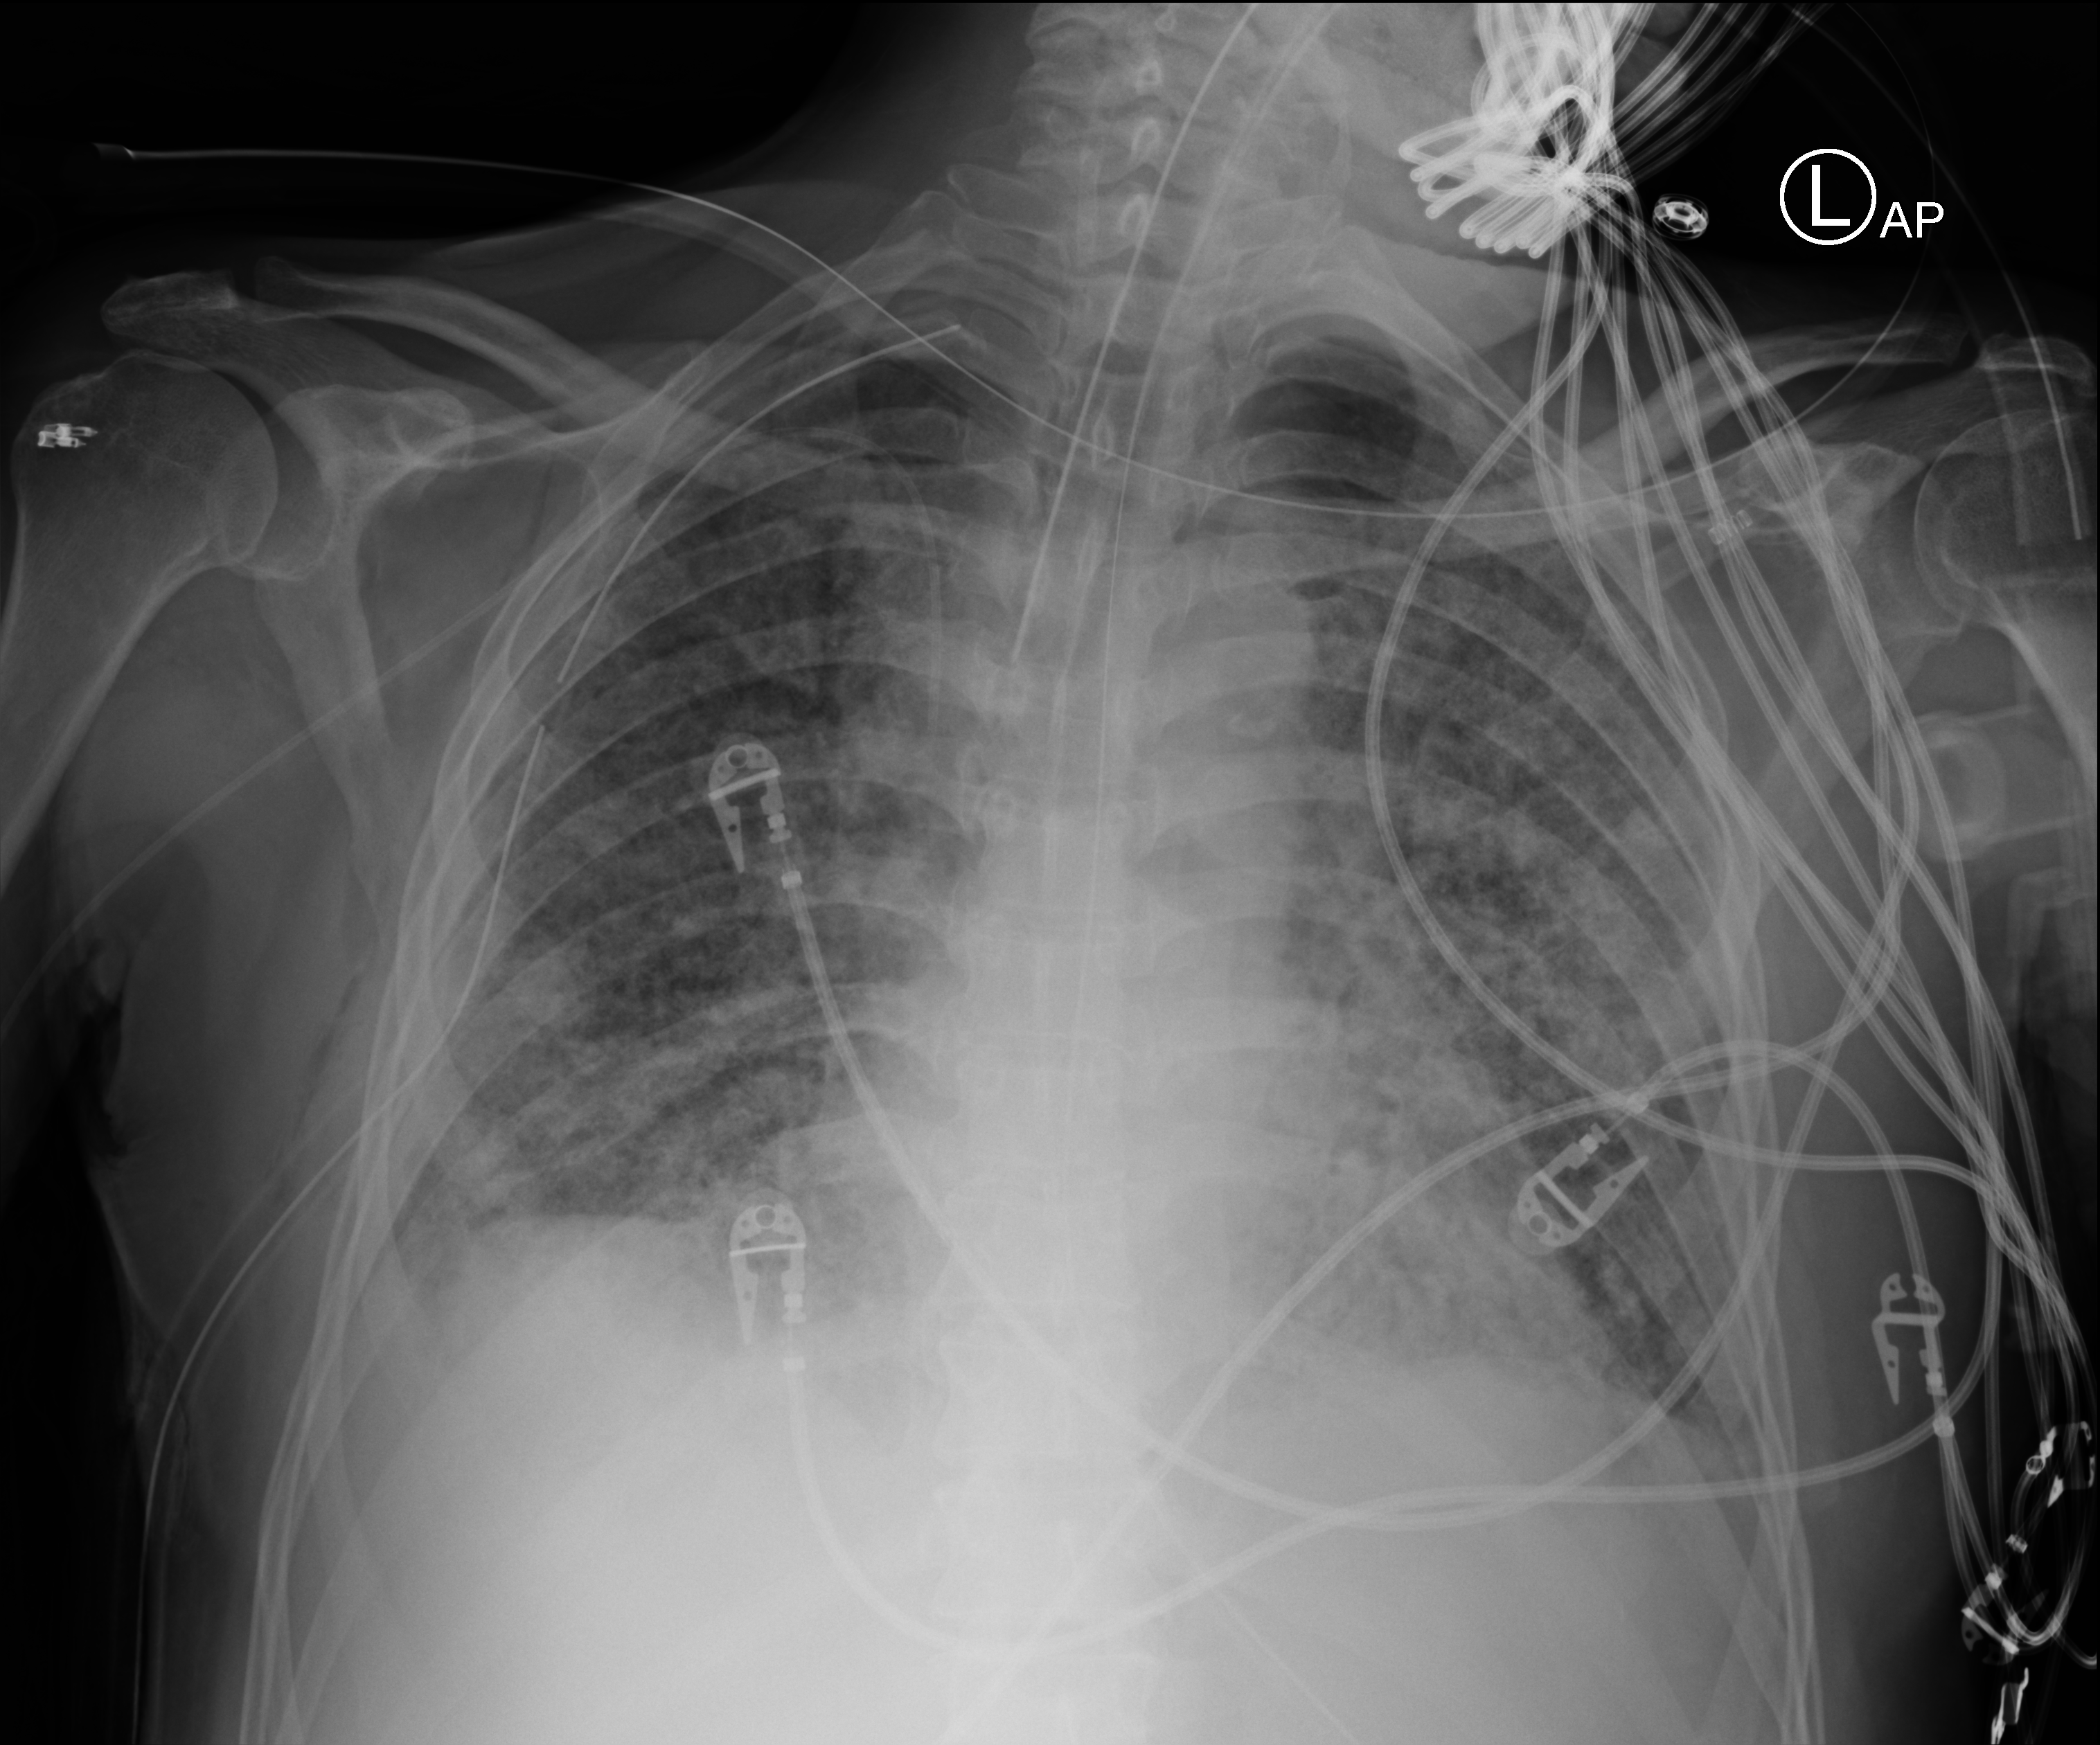
Portable chest radiograph; anteroposterior (AP) projection. Patient hospitalised with COVID-19; male, aged 60–74 years.
Admission-level facts for this patient (not findings on this image; timing relative to this image not recorded): other chronic lung disease (admission record): yes; diabetes (admission record): no; mechanically ventilated during this hospital stay: yes.